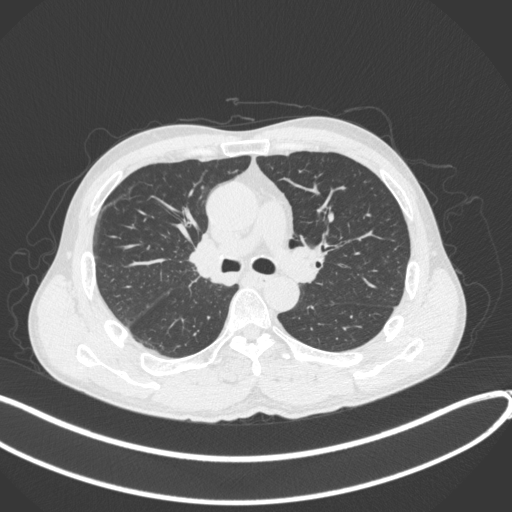
Chest CT, one axial slice; position 239 of 409 along the scan axis; reconstruction kernel B31f; lung window (W 1500 / L -600 HU); 1 mm slice thickness; 512 × 512 image matrix, field of view 400 × 400 mm. Patient: male, 53 years. Case-level facts recorded for this patient, not image findings: clinical TNM (as recorded): T1b N0 M0.
Outlined on this slice (bounding box drawn by a radiologist):
- lung tumour (recorded histology: squamous cell carcinoma): bounding box [x1, y1, x2, y2] px = [188, 228, 230, 282]